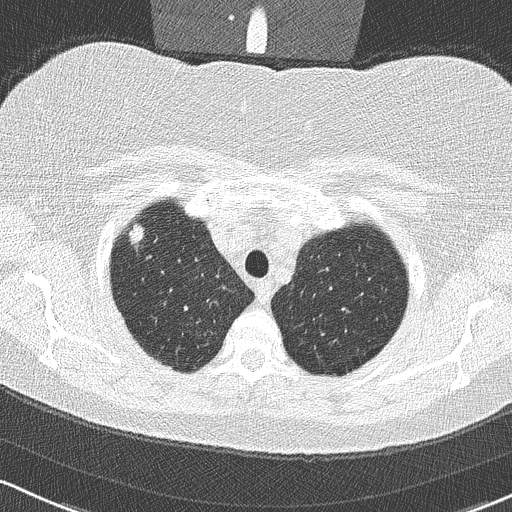
Chest CT (low-dose screening protocol), one axial image; third screening round (two years after baseline); lung window (W 1500 / L -600 HU); 2 mm slice thickness; lung (sharp) reconstruction kernel (B50f); slice 44 of 315 in the series; 512 × 512 image matrix, field of view 320 × 320 mm. Female, age 58 years at enrolment.
Expert-annotated lung lesion, bounding box [x1, y1, x2, y2] px = [118, 219, 158, 259]. The screening reader recorded 2 non-calcified nodules or masses ≥4 mm on this exam; which of them this box marks is not recorded. Official screen result: positive, other. Lung cancer was diagnosed 48 days after this screen: bronchiolo-alveolar adenocarcinoma, NOS, right upper lobe, well differentiated (G1), stage IA (AJCC 6th edition), 9 mm at pathology.